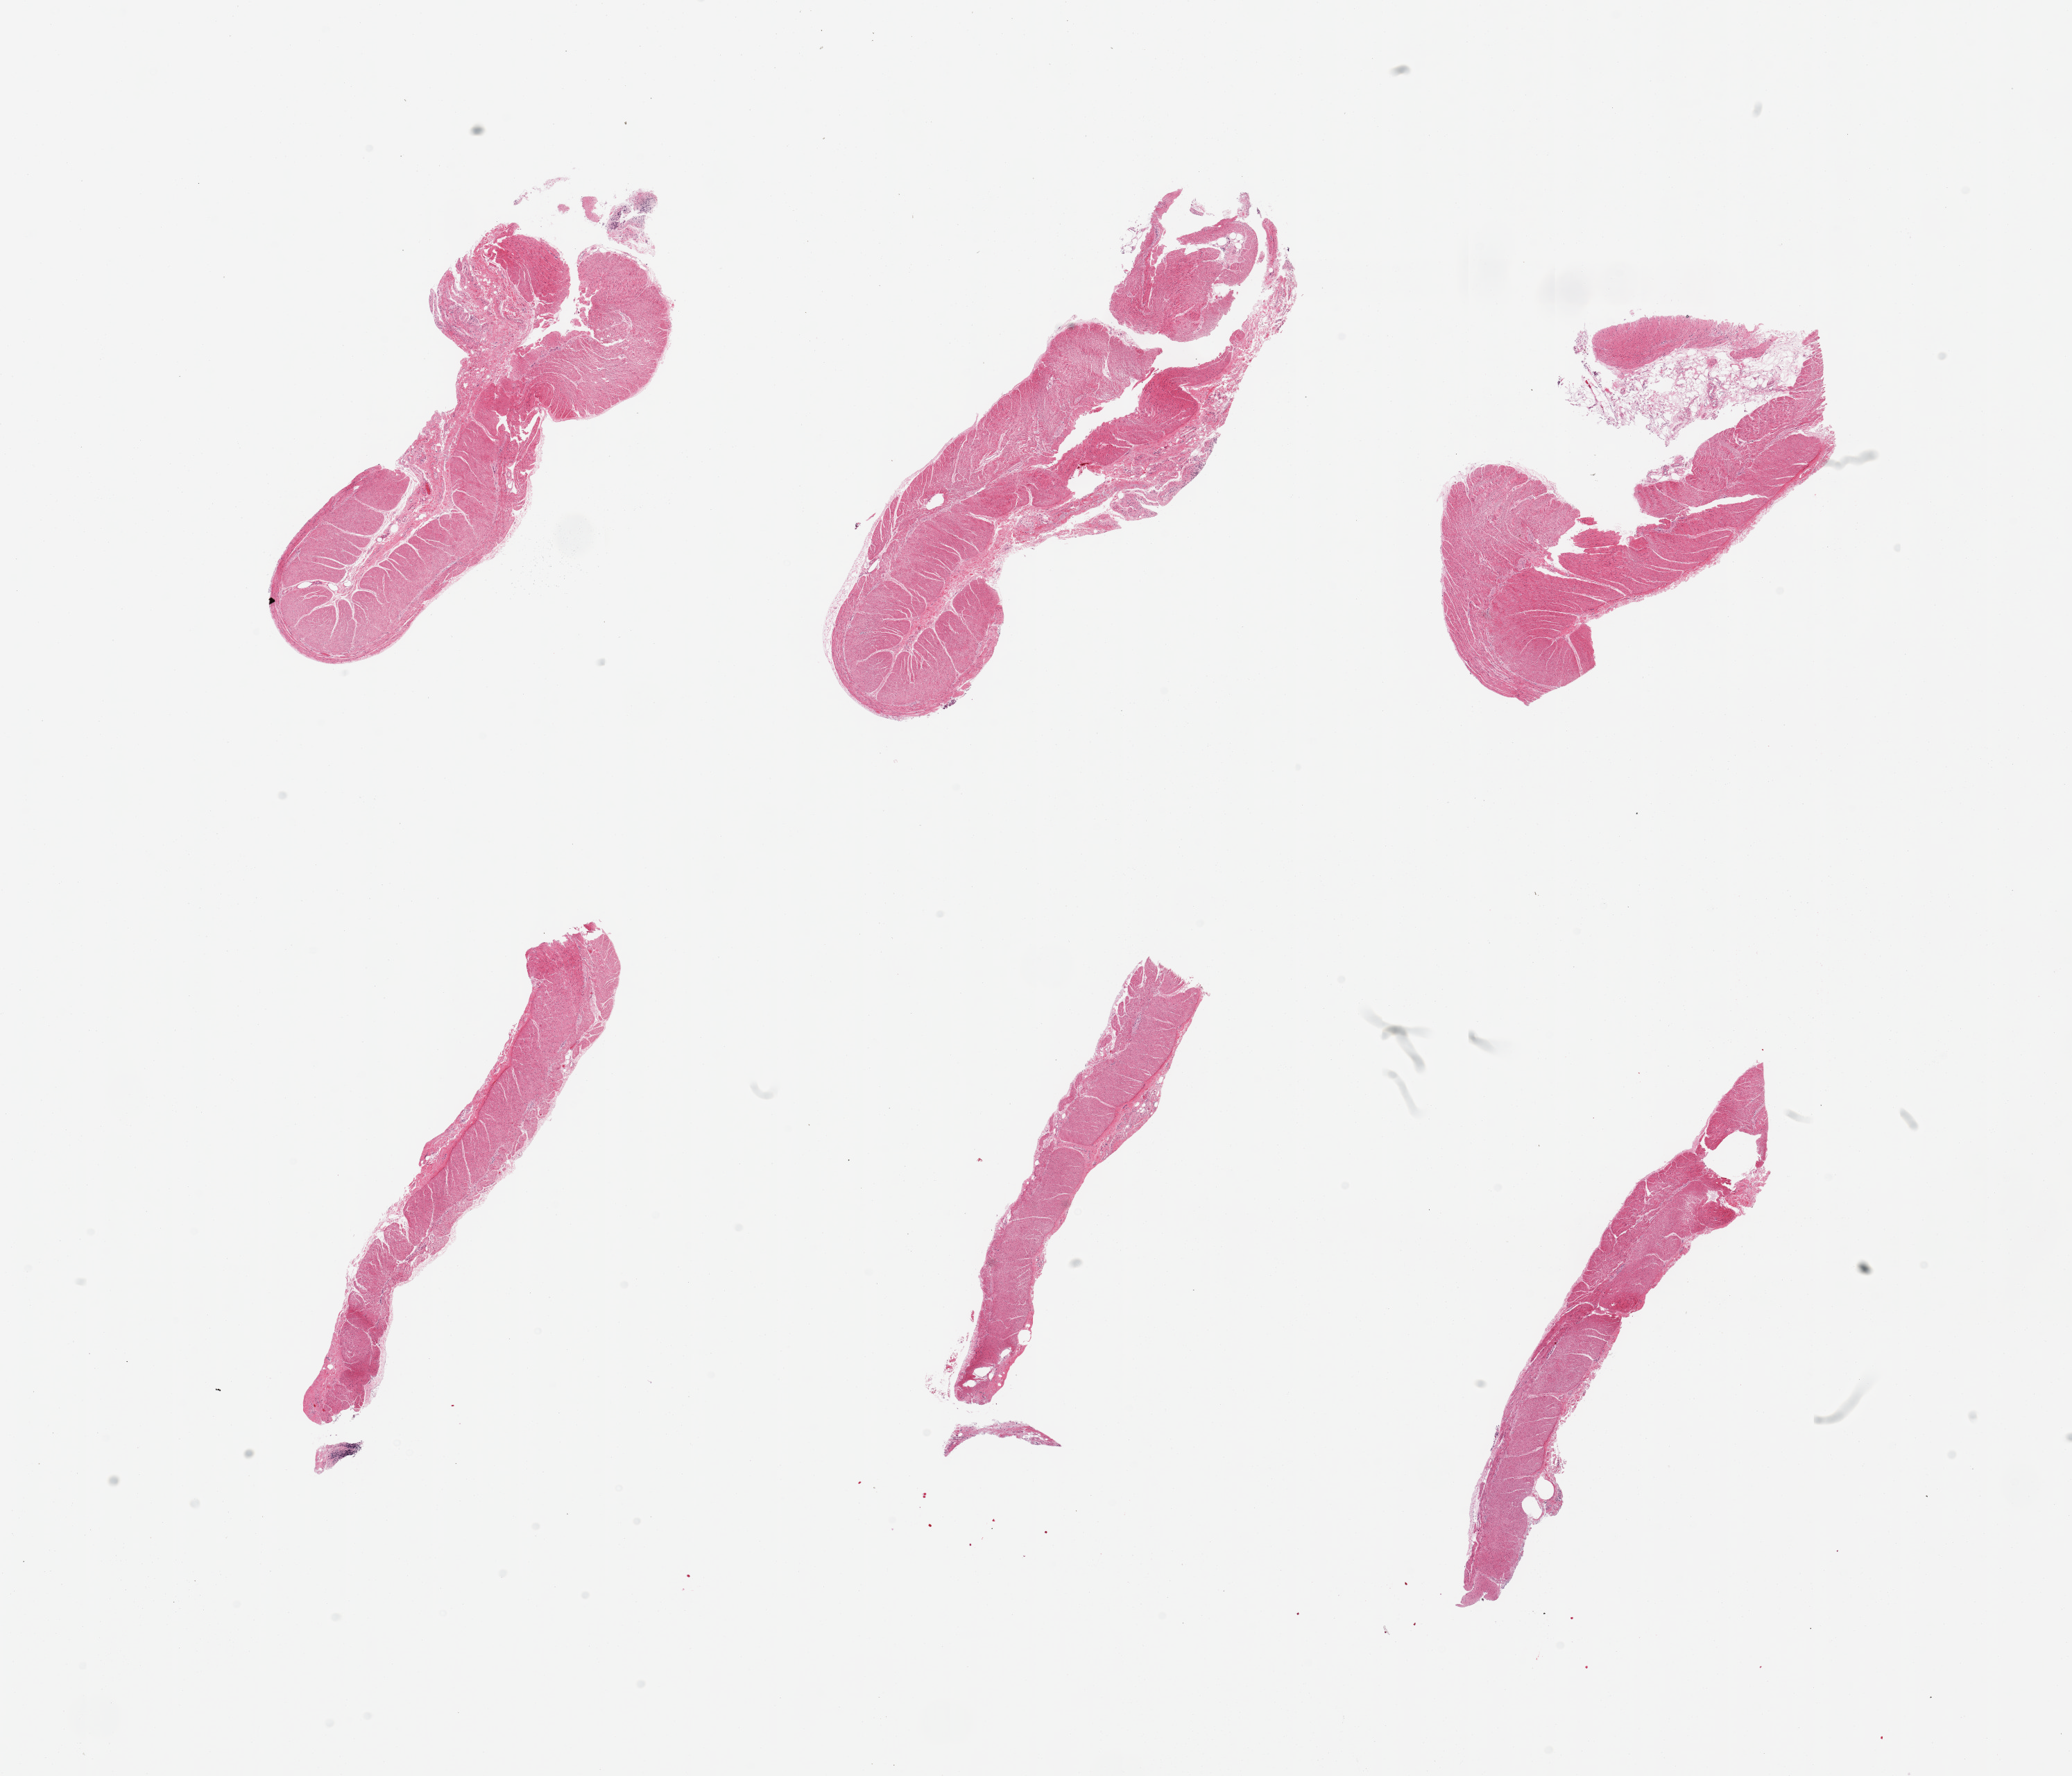
Digitized H&E-stained section, whole scanned area (about 23.6 x 20.2 mm) shown as a low-resolution overview, PAXgene-fixed, paraffin-embedded tissue, sampled site (target tissue): sigmoid colon, tissue donor sample. Donor sex: male.
Review note (as recorded): 6 pieces, confirmed target muscularis.